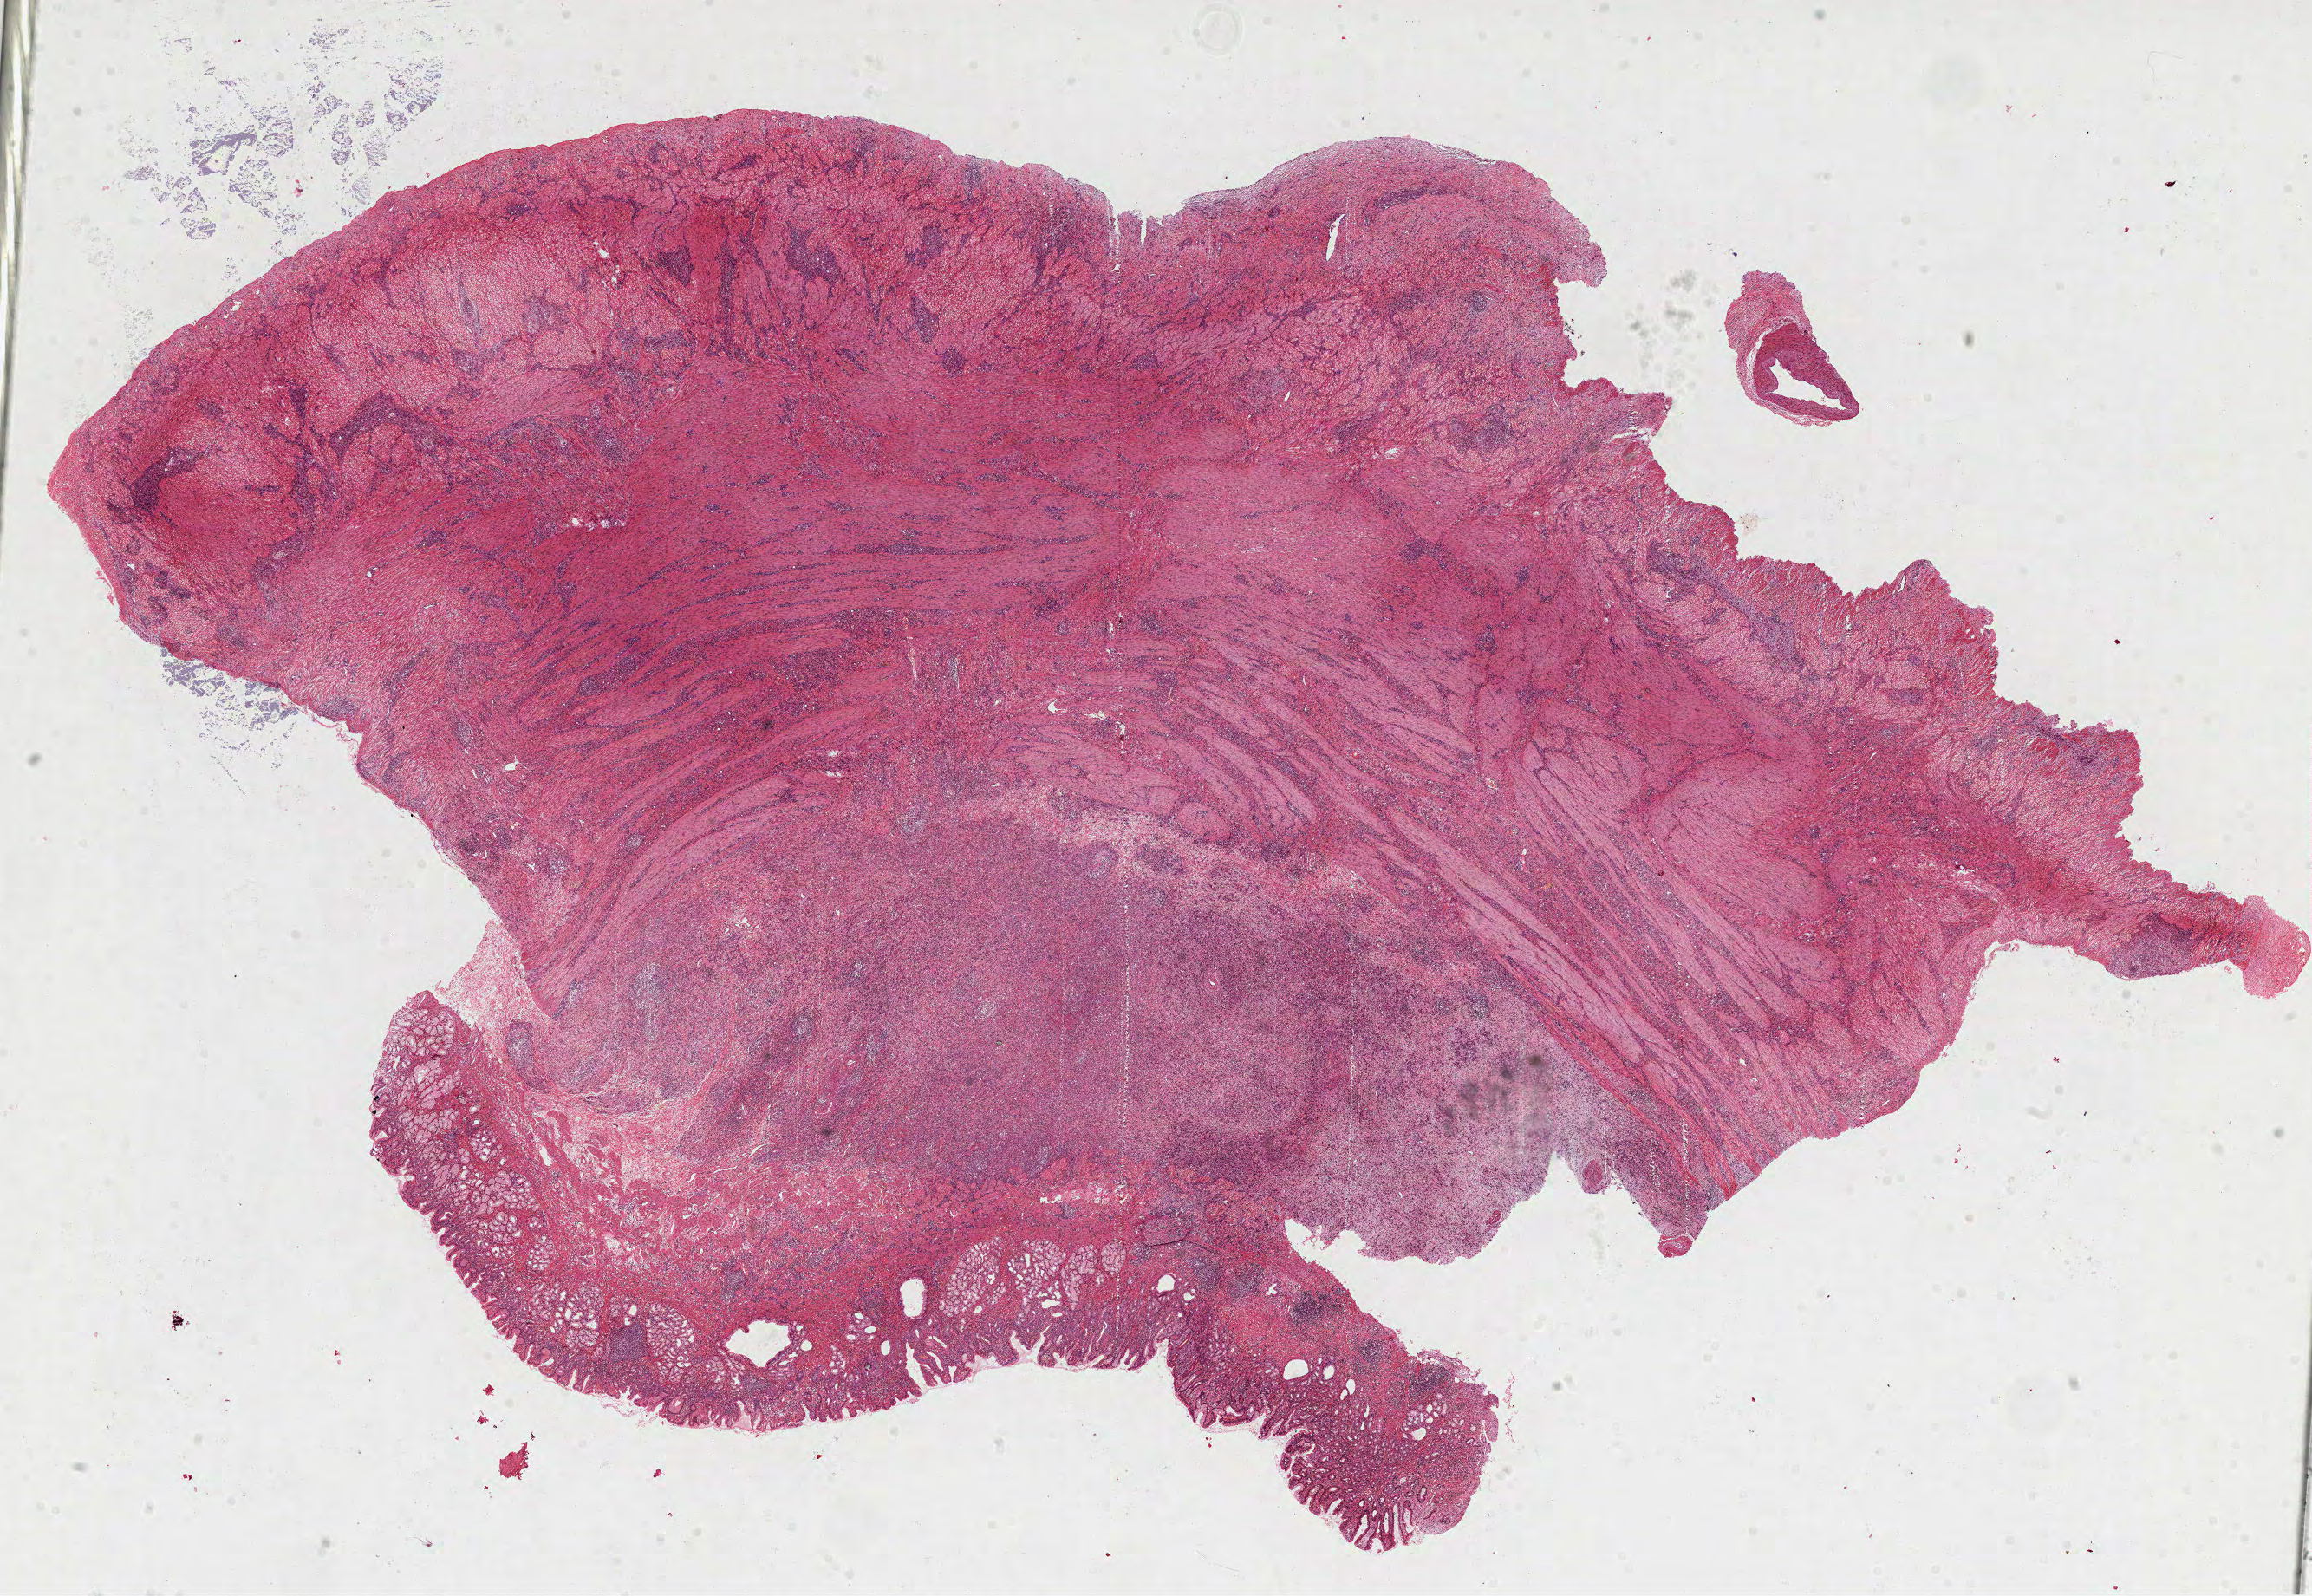
Whole-slide histology image, Hematoxylin and eosin (H&E) stained, shown as a low-resolution overview of the whole scanned area (about 21.5 x 14.9 mm, slide scanned at 40x). FFPE section. Sample: primary tumour, stomach. Patient: female, age at initial diagnosis 78 years. Histologic grade: G3 (poorly differentiated).
AJCC pathologic stage: II (6th edition). Histologic diagnosis: Adenocarcinoma, NOS.